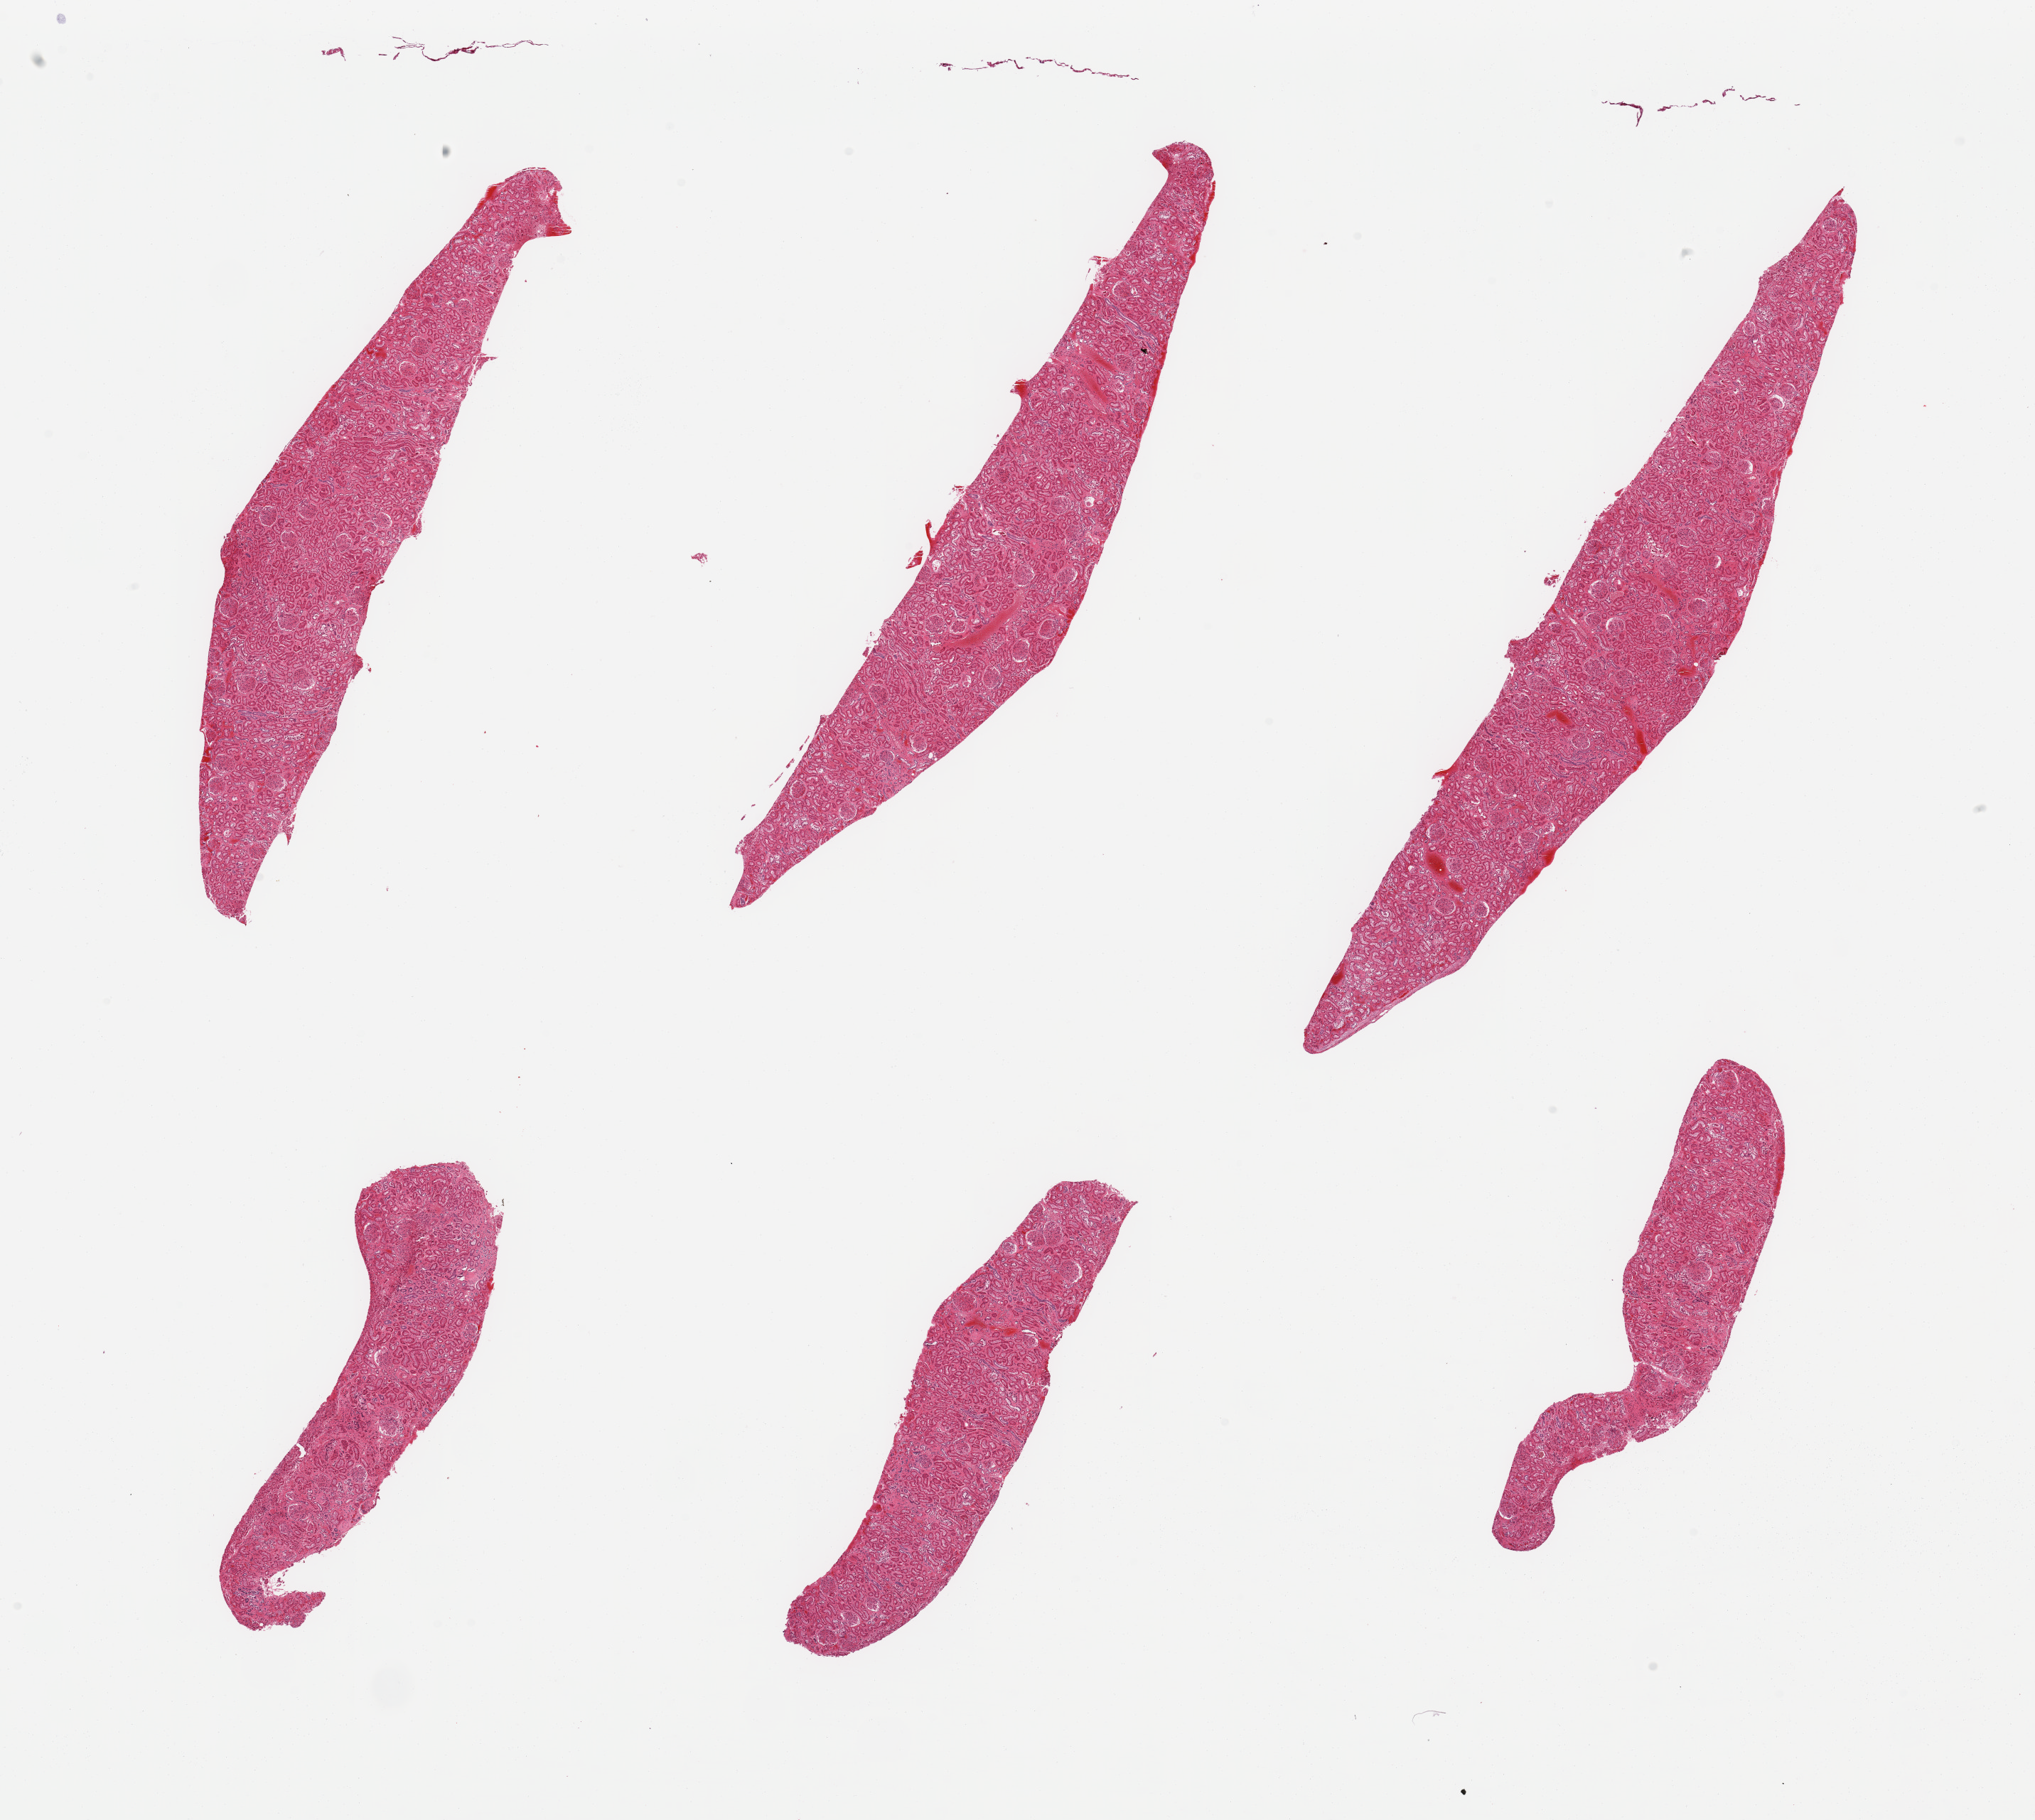
Whole-slide image, hematoxylin and eosin (H&E) stain — low-resolution overview of the scanned area, about 22.6 x 20.3 mm (slide scanned at 20x); PAXgene-fixed, paraffin-embedded tissue; target tissue: renal cortex; donor tissue sample. Donor: male.
Reviewer comment on this tissue sample: 6 pieces; no active or chronic lesions.